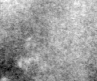
Region of interest cut from a scanned film mammogram (one marked finding), right breast, MLO view, BI-RADS breast density category 3 (scale 1–4).
Finding: calcifications, morphology pleomorphic, distribution clustered; BI-RADS assessment category 4; subtlety rating 3 on a 1 (subtle) to 5 (obvious) scale; pathology result (as recorded, not read from the image): malignant.